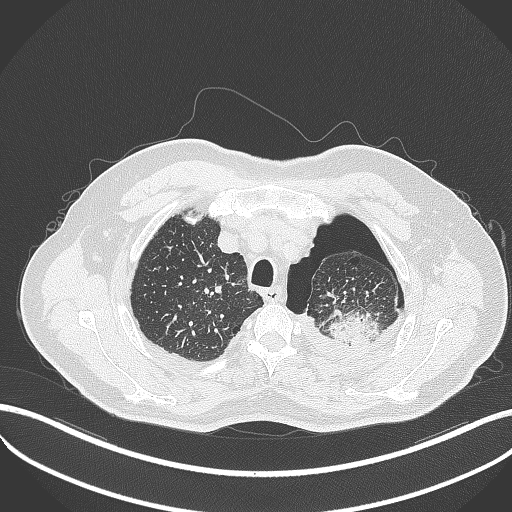
Chest CT, one axial slice. Position 415 of 464 along the scan axis. Reconstruction kernel B70f. 120 kVp. Lung window (W 1500 / L -600 HU). 512 × 512 image matrix, field of view 400 × 400 mm. Male patient, age 76 years. Case-level facts recorded for this patient, not image findings: clinical TNM (as recorded): T3 N0 M1b.
Annotated regions visible in this slice (rectangle marked by the reading radiologist):
- lung tumour (recorded histology: adenocarcinoma): box from (x=327, y=306) to (x=380, y=353) px